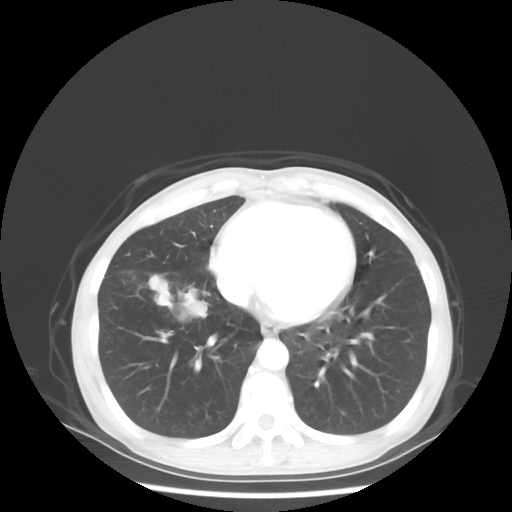
Chest CT, one axial slice; slice 18 of 56 in the series (ordered by position); reconstruction kernel STANDARD; 80 kVp; lung window (W 1500 / L -600 HU); 512 × 512 image matrix, field of view 360 × 360 mm. Female patient, age 57 years. Case-level facts recorded for this patient, not image findings: clinical TNM (as recorded): T1c N3 M1a.
Annotated regions visible in this slice (bounding box drawn by a radiologist):
- lung tumour (recorded histology: adenocarcinoma): box from (x=172, y=291) to (x=213, y=327) px